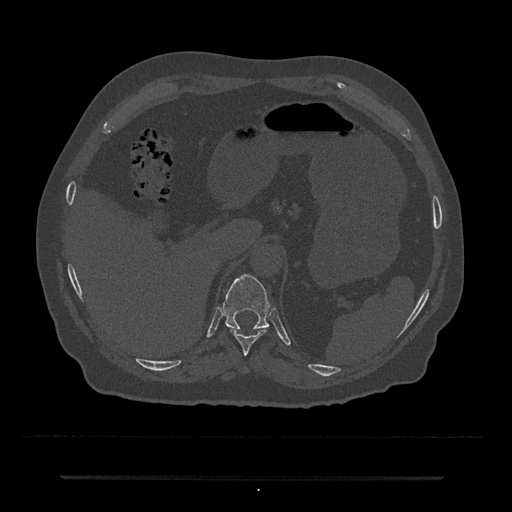
CT including the spine, one axial slice; position 203 of 797 along the scan axis; 120 kVp; bone window (W 1800 / L 400 HU); 0.5 mm slice thickness; 512 × 512 image matrix, field of view 437 × 437 mm. Patient: male, 69 years. From the clinical record (not read from this slice): primary cancer: prostate.
Outlined on this slice (semi-automatically segmented with operator editing):
- T10 vertebra: bounding box <230,329,266,355> (left, top, right, bottom; pixels)
- T11 vertebra: <222,274,270,330>